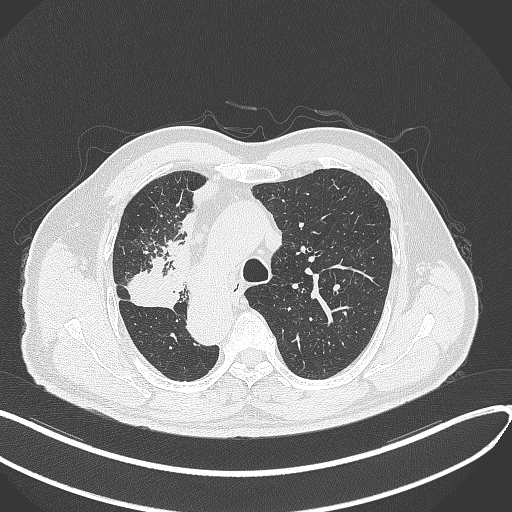
Chest CT, one axial slice. Position 225 of 300 along the scan axis. Reconstruction kernel B70f. Lung window (W 1500 / L -600 HU). 512 × 512 image matrix. Patient: male, 67 years. Case-level facts recorded for this patient, not image findings: clinical TNM (as recorded): T2a N0 M0.
Annotated regions visible in this slice (rectangle marked by the reading radiologist):
- lung tumour (recorded histology: squamous cell carcinoma): box from (x=122, y=255) to (x=188, y=311) px